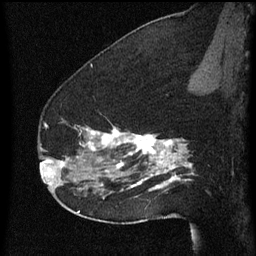
Breast MRI (dynamic contrast-enhanced), one sagittal slice. Slice 41 of 60 in the series (ordered by position). Dynamic contrast-enhanced series, image 2 of 3 at this slice position (ordered by acquisition). 1.5 T. TE 4.2 ms, TR 8 ms. 2 mm slice thickness. 256 × 256 image matrix. Female patient, age 52 years.
Outlined on this slice (semi-automatic segmentation, software-assisted and operator-edited):
- analysis volume of interest (the breast-tissue region the enhancement analysis was run in; not a lesion): bounding box <54,114,178,207> (left, top, right, bottom; pixels)
- tumour enhancement mask (voxels above the 70 % enhancement threshold inside the analysis volume of interest): <61,126,178,191>